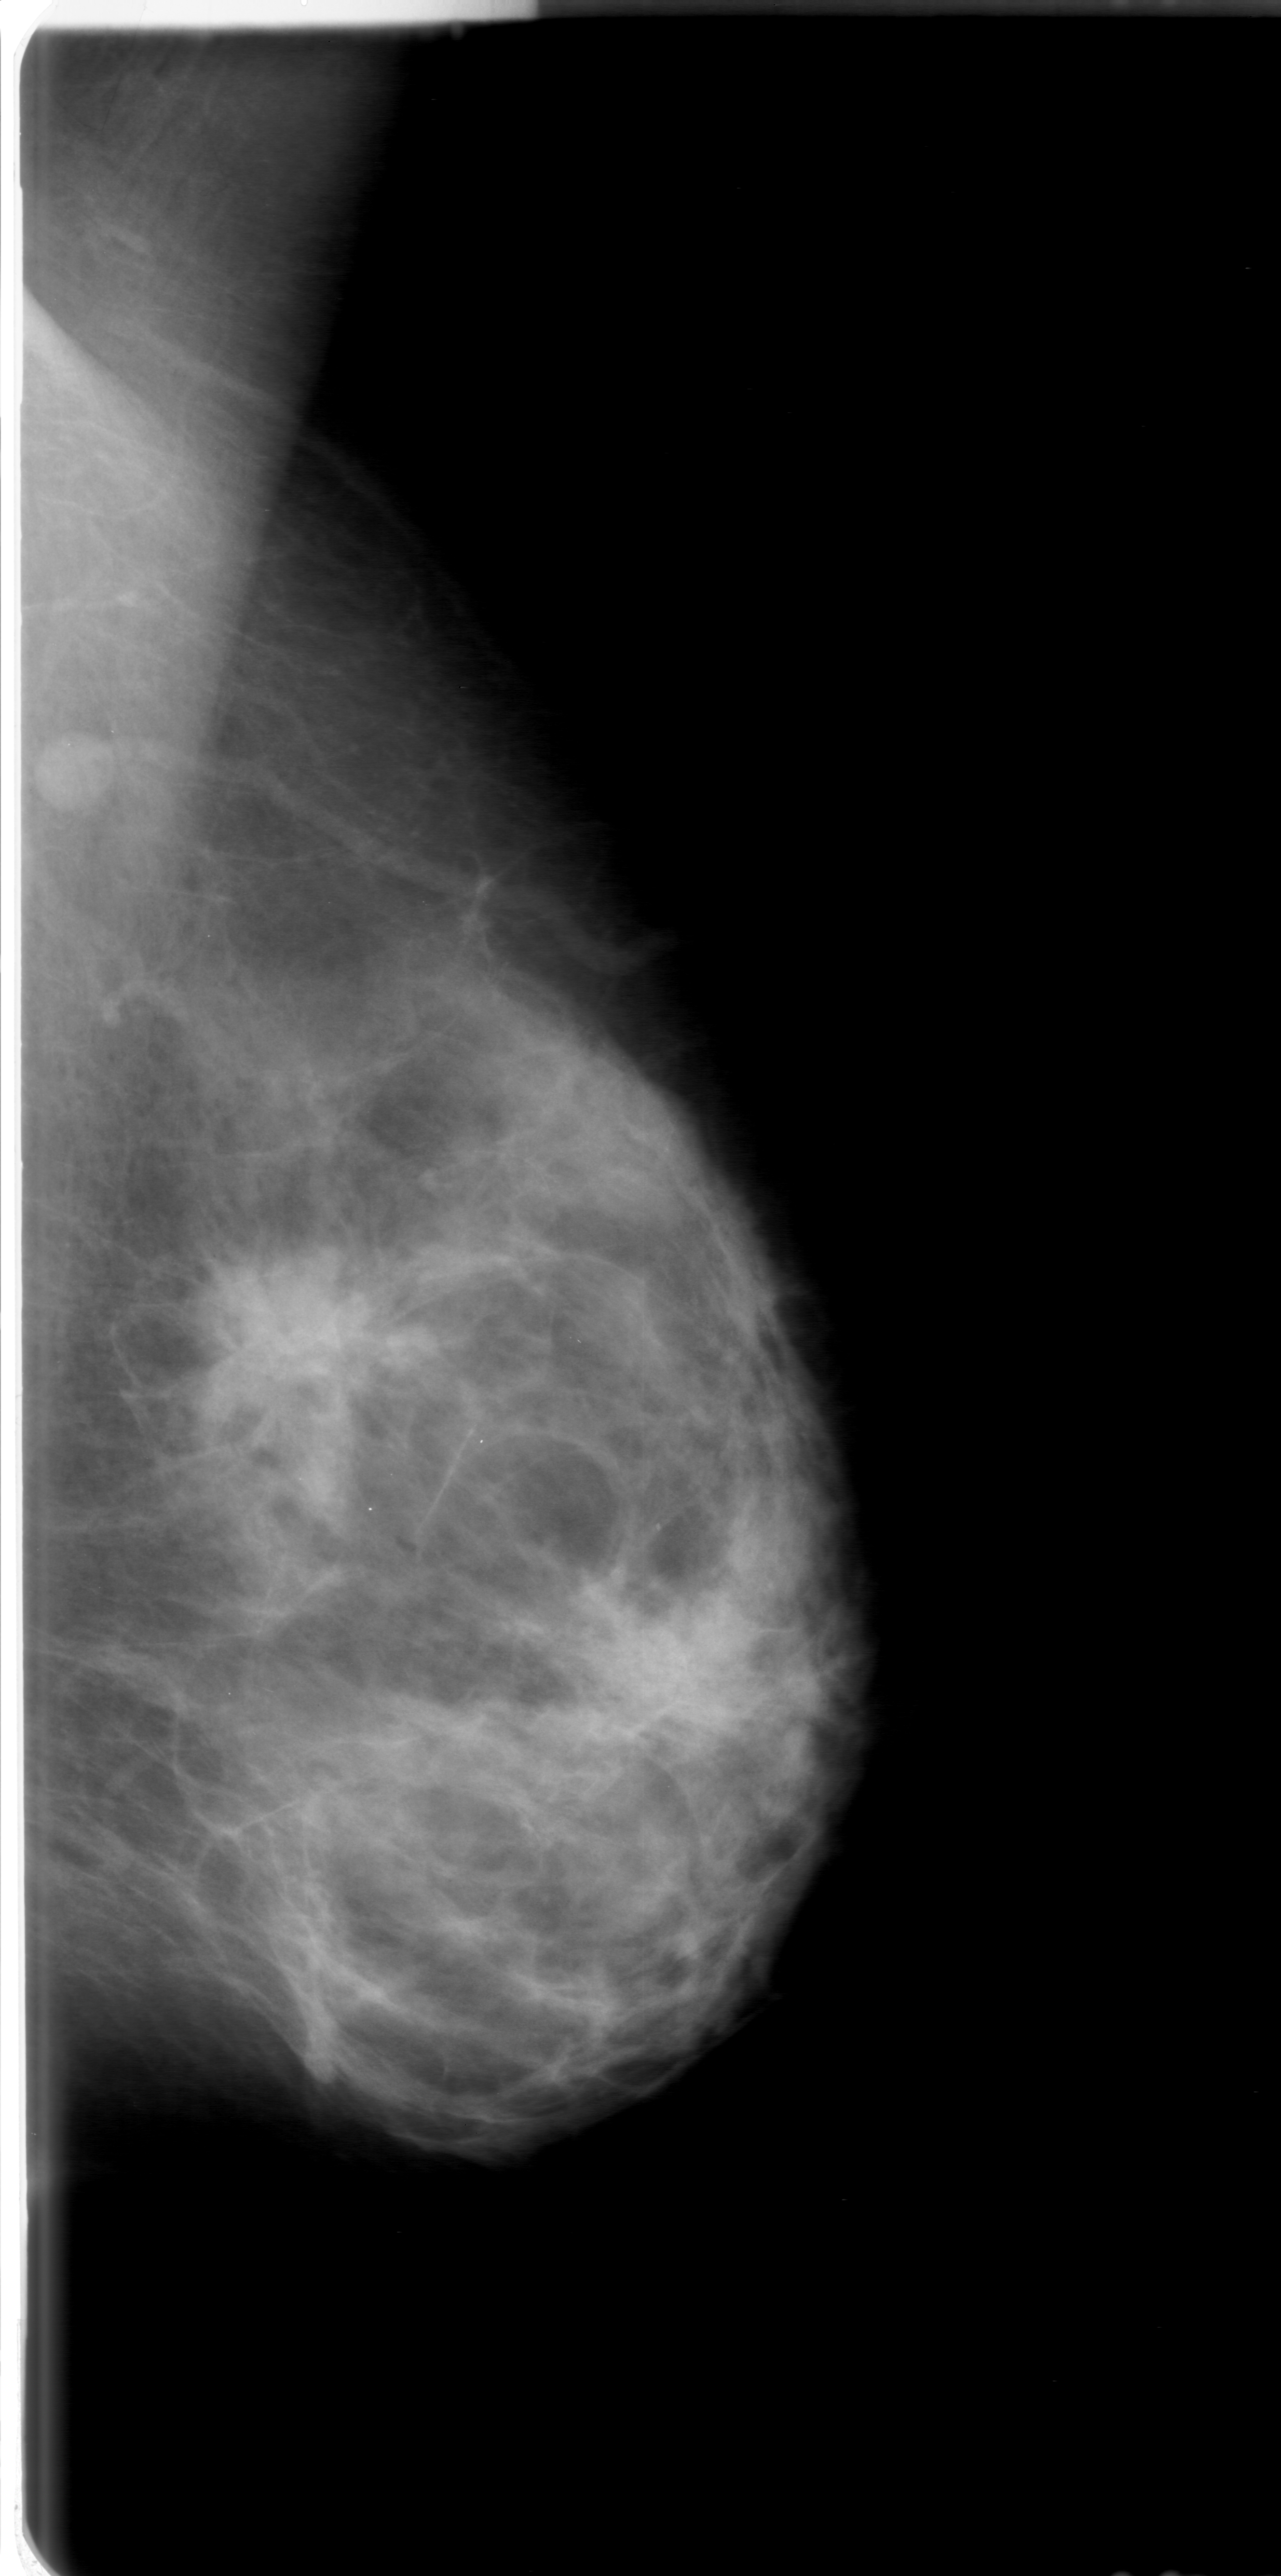
Mammogram (digitized film); left breast; MLO view; BI-RADS breast density category 3 (scale 1–4).
Mass, shape irregular, margins spiculated; BI-RADS assessment category 5; subtlety rating 4 on a 1 (subtle) to 5 (obvious) scale; pathology result (as recorded, not read from the image): malignant.